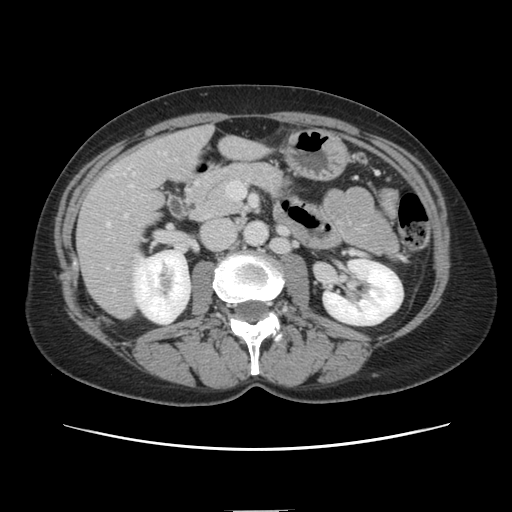
Contrast-enhanced abdominal CT, one axial slice; position 50 of 141 along the scan axis; 120 kVp; intravenous contrast given; soft-tissue window (W 400 / L 40 HU); 2.5 mm slice thickness; 512 × 512 image matrix, field of view 350 × 350 mm. Female patient, age 63 years. Case-level facts recorded for this patient, not image findings: diagnosis: colorectal cancer liver metastases, imaged before liver resection; multiple liver metastases: yes; largest metastasis: 3.2 cm; chemotherapy before resection: yes.
Outlined on this slice (manually delineated by an expert):
- liver: bounding box <78,128,262,318> (left, top, right, bottom; pixels)
- planned liver remnant (the part of the liver to remain after resection): <179,128,262,171>